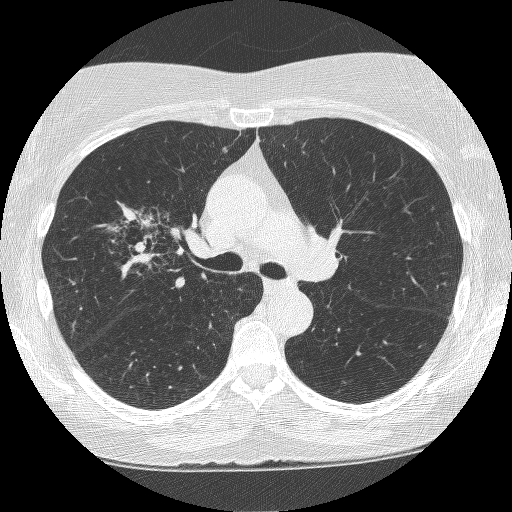
Axial slice from a low-dose chest CT screening exam. Second annual screen. Lung window (W 1500 / L -600 HU). 1.25 mm slice thickness. Lung (sharp) reconstruction kernel (BONE). 120 kVp. 512 × 512 image matrix. Female participant, aged 64 years at enrolment.
• Lesion marked by an expert reader, box from (x=115, y=205) to (x=207, y=291) px.
• The screening reader recorded 4 non-calcified nodules or masses ≥4 mm on this exam (right upper lobe, right upper lobe, right upper lobe, left upper lobe); which of them this box marks is not recorded.
• Official screen result: positive, other.